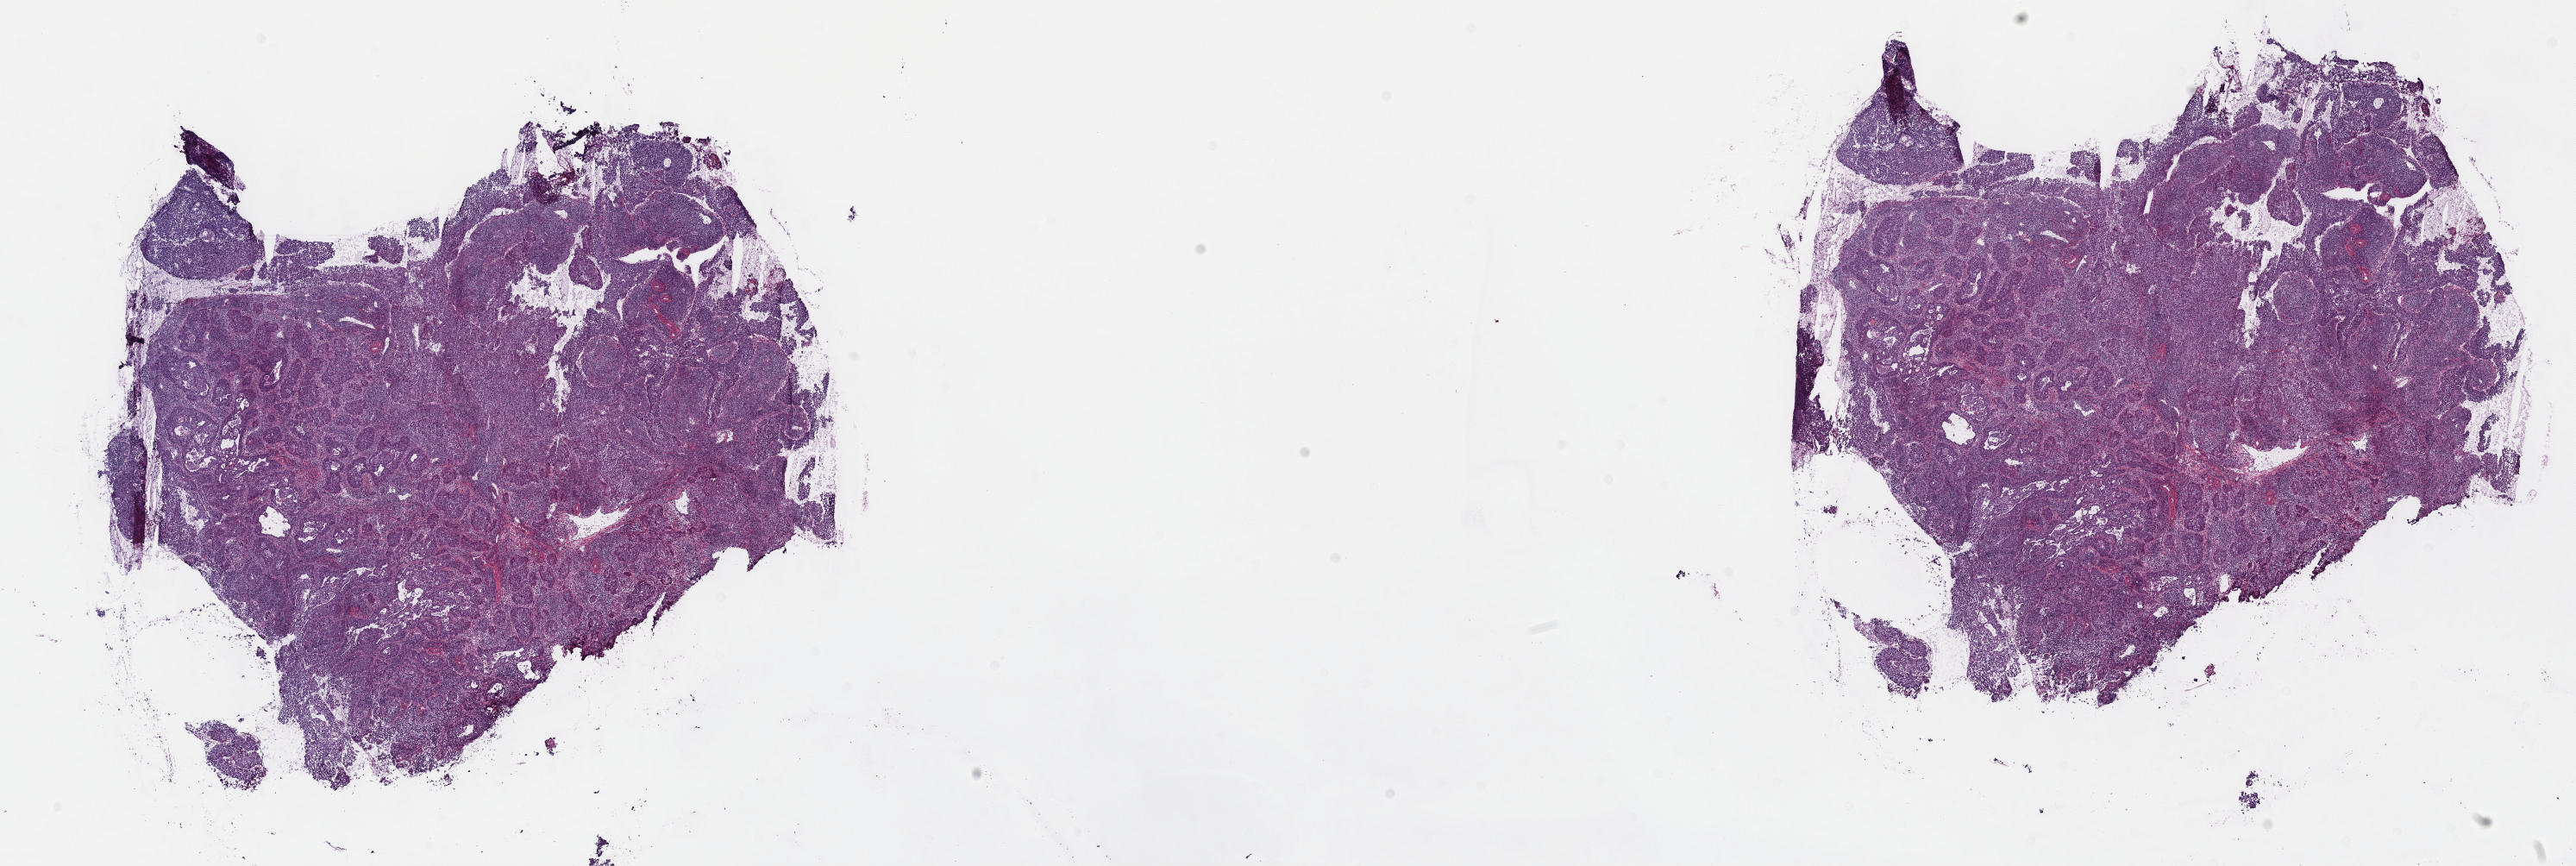
Digitized H&E tissue section (whole slide), shown as a low-resolution overview of the whole scanned area (about 24.2 x 8.1 mm, acquisition: 40x scan); frozen section from the top of the tissue portion; primary tumour sample from the cervix. Female, age 57 years at initial diagnosis. Histologic grade: G3 (poorly differentiated). Composition of this section per pathologist review: tumour cells 60%, tumour nuclei 60%, normal cells 35%, stromal cells 5%, necrosis 0%. Infiltration values recorded for this section: lymphocyte infiltration 35%, monocyte infiltration 0%, neutrophil infiltration 0%.
* diagnosis: Squamous cell carcinoma, NOS
* FIGO stage: IIB